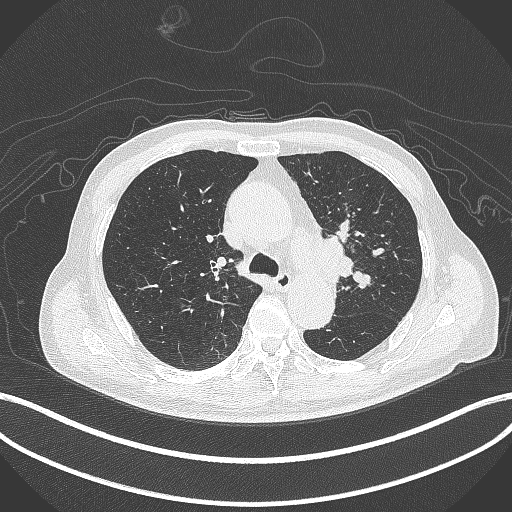
Chest CT, one axial slice; slice 297 of 417 in the series (ordered by position); reconstruction kernel B70f; 120 kVp; lung window (W 1500 / L -600 HU); 1 mm slice thickness; 512 × 512 image matrix, field of view 400 × 400 mm. Patient: male, 77 years. Case-level facts recorded for this patient, not image findings: clinical TNM (as recorded): T3 N1 M0.
Structures marked on this image (bounding box drawn by a radiologist):
- lung tumour (recorded histology: adenocarcinoma): bounding box (x1, y1, x2, y2) in pixels: (317, 233, 358, 281)